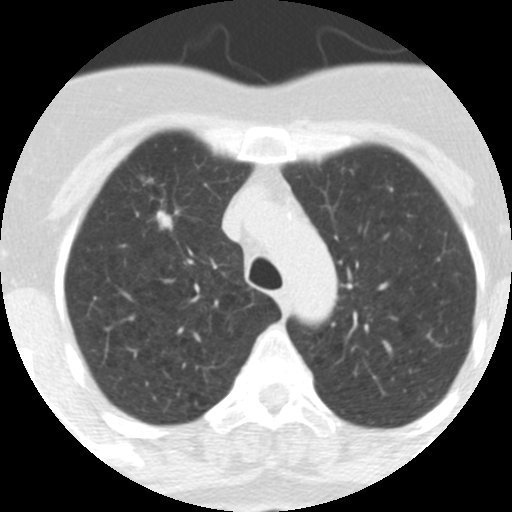
Low-dose screening chest CT, one axial slice. Slice 243 of 313 in the series (ordered by position). Reconstruction kernel STANDARD. 120 kVp. Lung window (W 1500 / L -600 HU). 2.5 mm slice thickness. 512 × 512 image matrix.
Outlined on this slice (expert manual segmentation):
- lesion 1 (tumor, upper lobe of right lung): box from (x=156, y=210) to (x=179, y=230) px